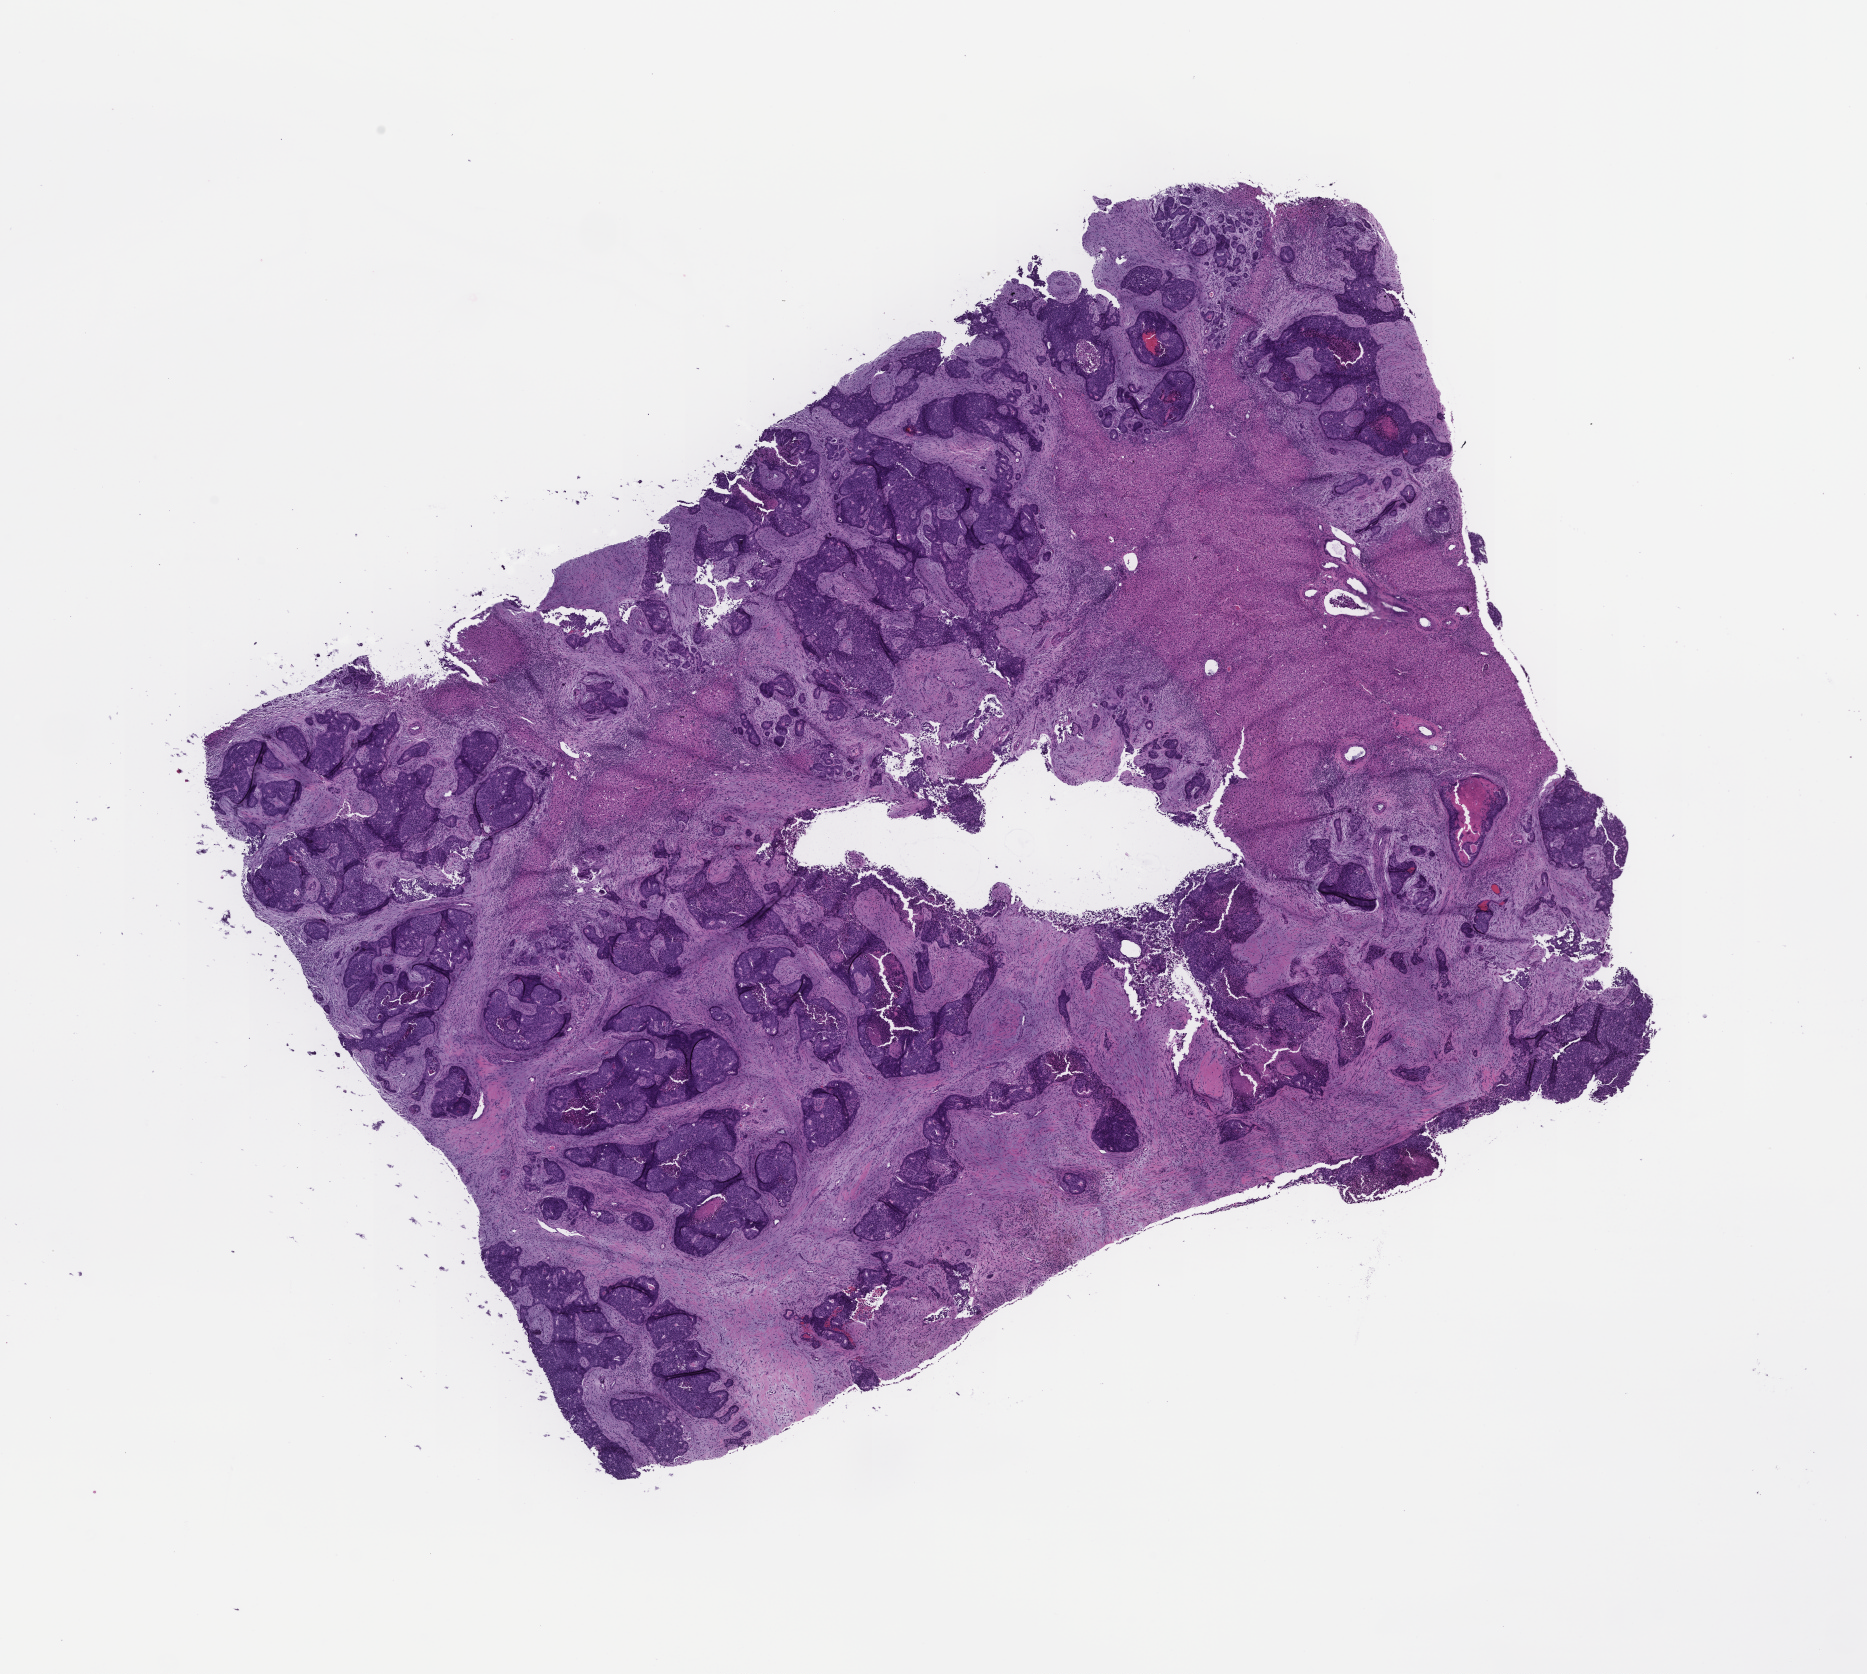
Digitized hematoxylin and eosin (H&E)-stained section, a low-resolution overview of the entire scanned area, about 15.1 x 13.5 mm, formalin-fixed paraffin-embedded section, specimen time point: collected on treatment. Patient: female.
This section: metastatic tumor tissue. Primary diagnosis of the patient: Colorectal Carcinoma.